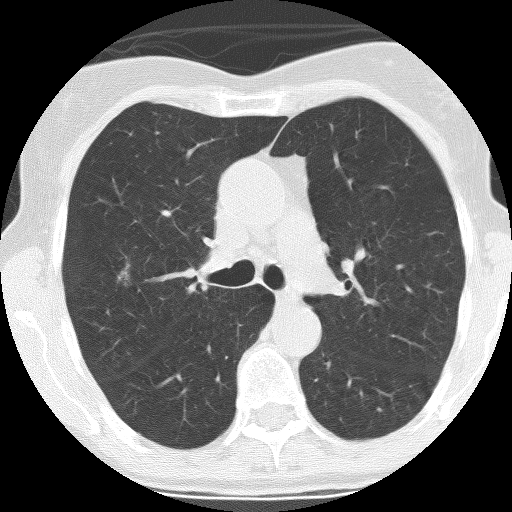
Low-dose screening chest CT, one axial slice. Slice 172 of 261 in the series (ordered by position). Reconstruction kernel BONE. Lung window (W 1500 / L -600 HU). 2.5 mm slice thickness. 512 × 512 image matrix, field of view 270 × 270 mm.
Annotated regions visible in this slice (manually delineated by an expert):
- lesion 1 (tumor, upper lobe of right lung): bounding box (x1, y1, x2, y2) in pixels: (118, 268, 130, 280)